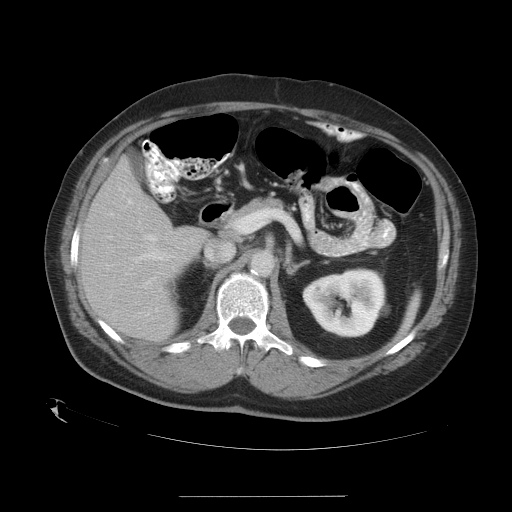
Contrast-enhanced abdominal CT, one axial slice; reconstruction kernel STANDARD; 120 kVp; soft-tissue window (W 400 / L 40 HU); 7.5 mm slice thickness; 512 × 512 image matrix, field of view 450 × 450 mm. Male patient, age 67 years. From the clinical record (not read from this slice): diagnosis: colorectal cancer liver metastases, imaged before liver resection; multiple liver metastases: no; largest metastasis: 2.3 cm; chemotherapy before resection: no.
Annotated regions visible in this slice (outlined manually by an expert reader):
- hepatic veins: bounding box <128,199,132,204> (left, top, right, bottom; pixels)
- liver: <83,162,203,340>
- planned liver remnant (the part of the liver to remain after resection): <83,162,202,340>
- portal vein (with intrahepatic branches): <134,223,239,286>